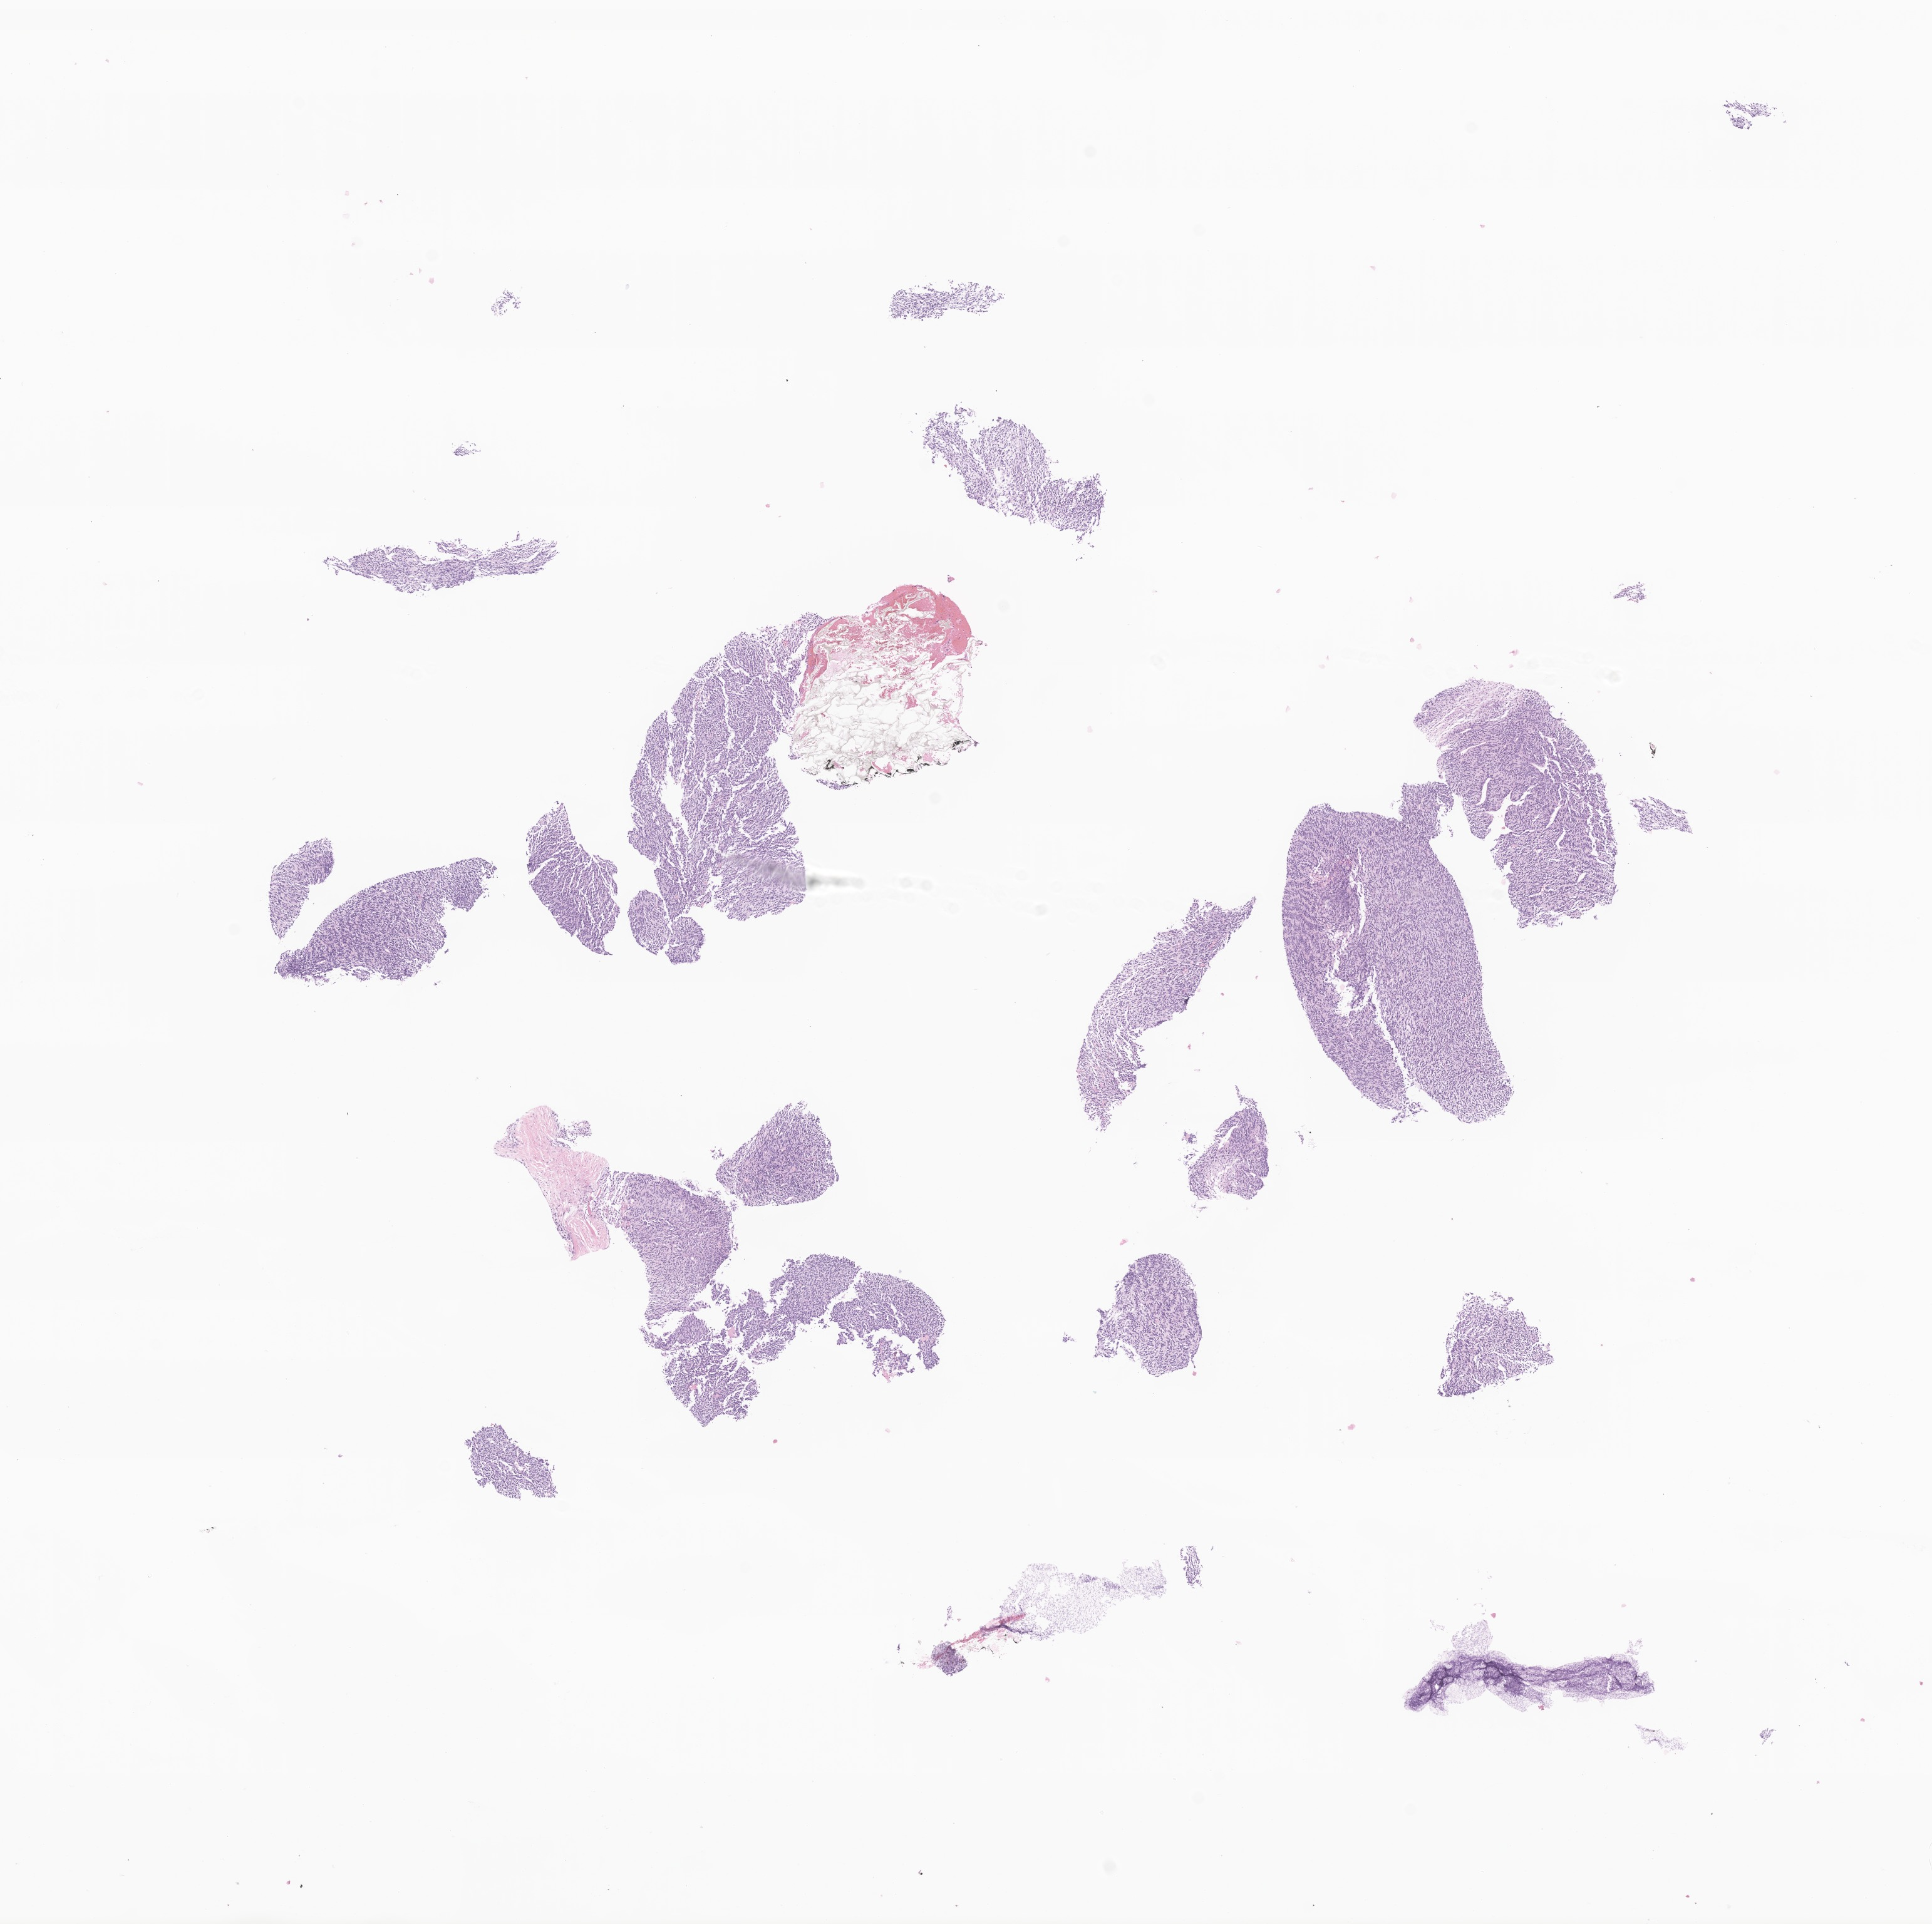
Hematoxylin and eosin (H&E) whole-slide image of tumor tissue from the soft tissue of upper extremity, whole scanned area (about 13.0 x 13.0 mm) shown as a low-resolution overview; formalin-fixed, paraffin-embedded (FFPE) tissue. Female patient, age 237 months (19 years 9 months).
* diagnosis (ICD-O-3 morphology term): Neoplasm, uncertain whether benign or malignant